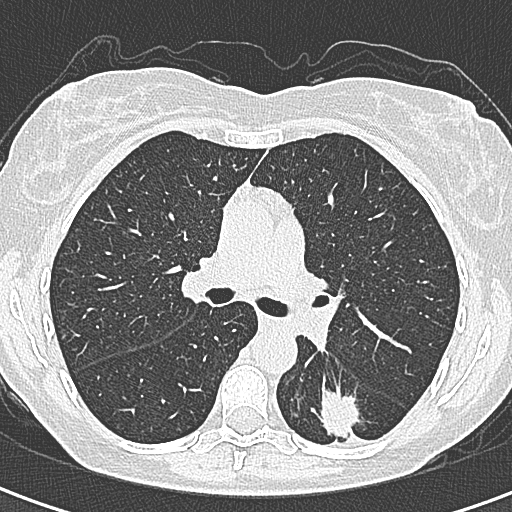
Axial slice from a low-dose chest CT screening exam; baseline annual screen; lung window (W 1500 / L -600 HU); 1 mm slice thickness; 512 × 512 image matrix, field of view 284 × 284 mm. Female, age 58 years at enrolment.
Expert-annotated lung lesion, bounding box (x1, y1, x2, y2) in pixels: (293, 389, 363, 455). The screening reader recorded 2 non-calcified nodules or masses ≥4 mm on this exam; which of them this box marks is not recorded. Participant outcome: lung cancer diagnosed 22 days after this screen — adenocarcinoma, NOS, left lower lobe, moderately differentiated (G2), stage IA (AJCC 6th edition), 25 mm at pathology.